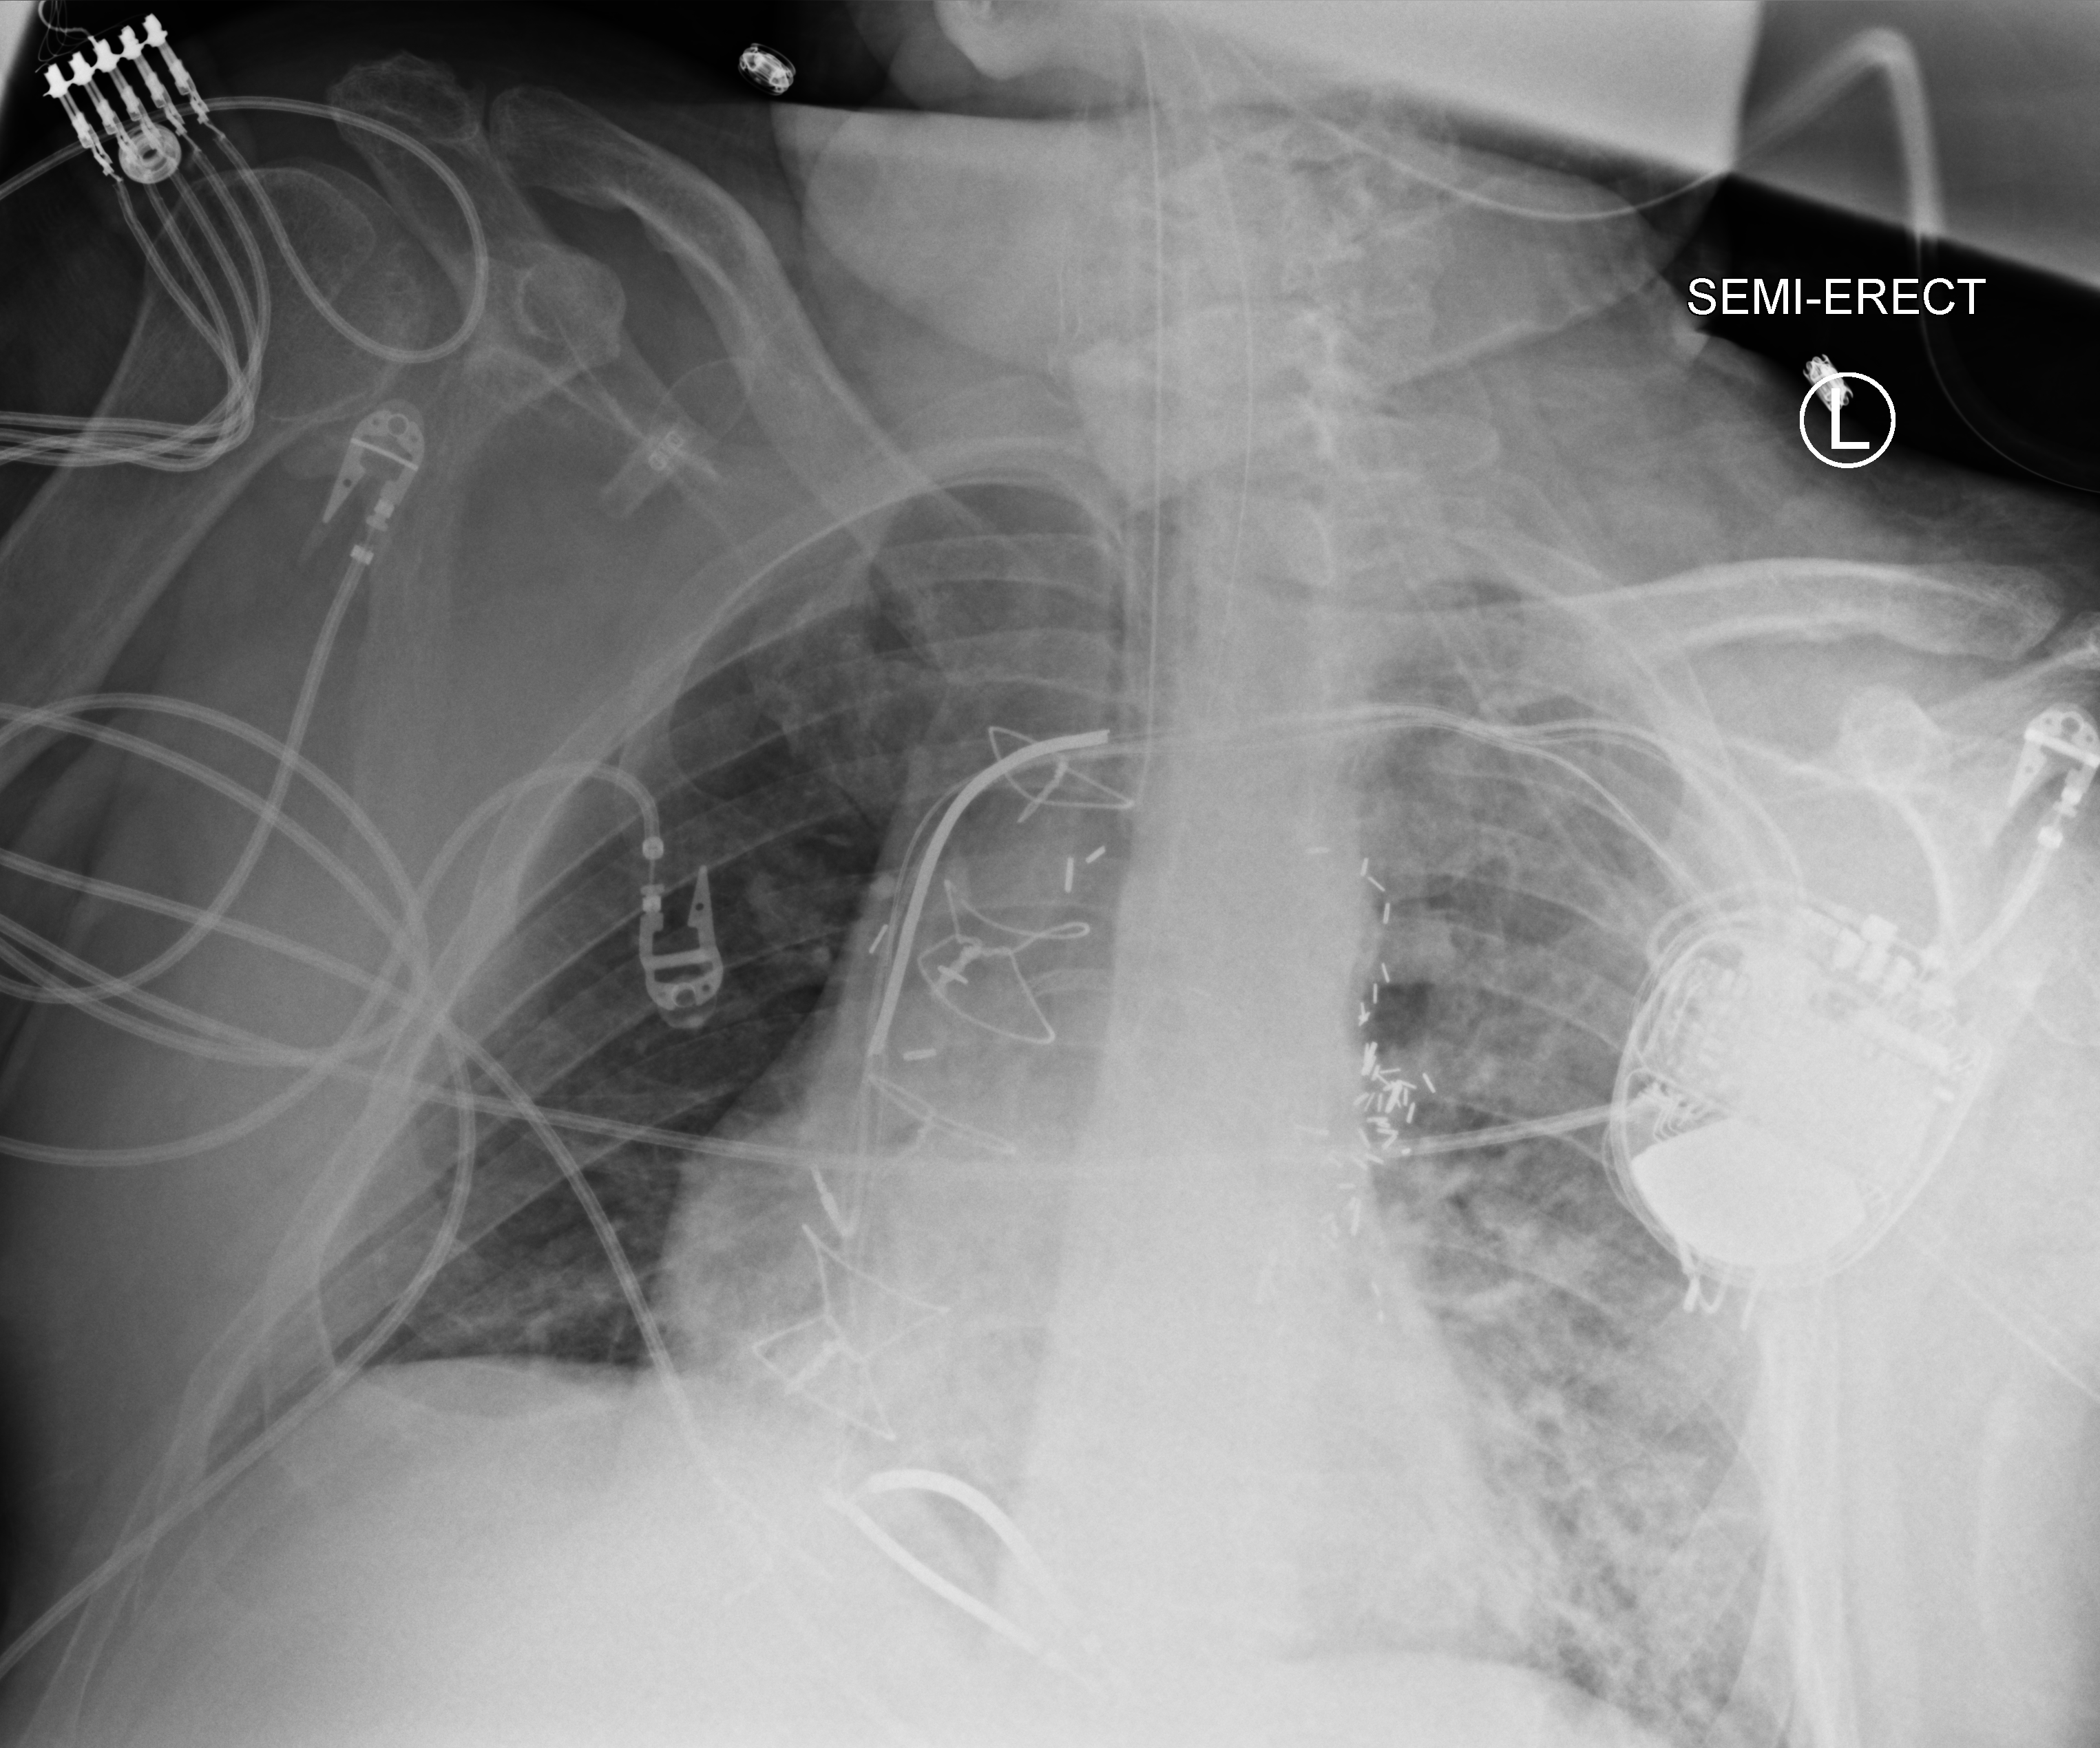
Portable chest radiograph; anteroposterior (AP) projection. Patient hospitalised with COVID-19; male, aged 60–74 years.
From the hospital-stay record, not from the radiograph (when in the stay this image was taken is not recorded): mechanically ventilated during this hospital stay: yes; admitted to intensive care during this hospital stay: yes.